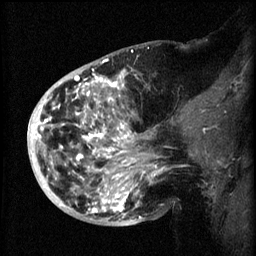
Breast MRI (dynamic contrast-enhanced), one sagittal slice. Slice 23 of 60 in the series (ordered by position). 3 images stored at this slice position (order not interpretable as contrast timing). 1.5 T. TE 4.2 ms, TR 8.2 ms. 2 mm slice thickness. 256 × 256 image matrix. Patient: female, 50 years.
Outlined on this slice (semi-automatically segmented with operator editing):
- analysis volume of interest (the breast-tissue region the enhancement analysis was run in; not a lesion): bounding box <44,72,163,219> (left, top, right, bottom; pixels)
- tumour enhancement mask (voxels above the 70 % enhancement threshold inside the analysis volume of interest): <44,74,162,215>